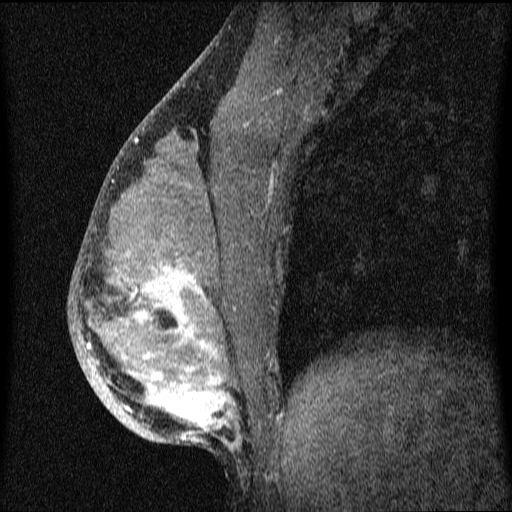
Breast MRI (dynamic contrast-enhanced), one sagittal slice. Position 29 of 64 along the scan axis. Dynamic contrast-enhanced series, image 2 of 4 at this slice position (ordered by acquisition). 1.5 T. TE 4.2 ms, TR 9.1 ms. 2 mm slice thickness. 512 × 512 image matrix. Female patient, age 33 years.
Annotated regions visible in this slice (semi-automatic segmentation, software-assisted and operator-edited):
- analysis volume of interest (the breast-tissue region the enhancement analysis was run in; not a lesion): bounding box <69,151,336,458> (left, top, right, bottom; pixels)
- tumour enhancement mask (voxels above the 70 % enhancement threshold inside the analysis volume of interest): <87,196,235,447>